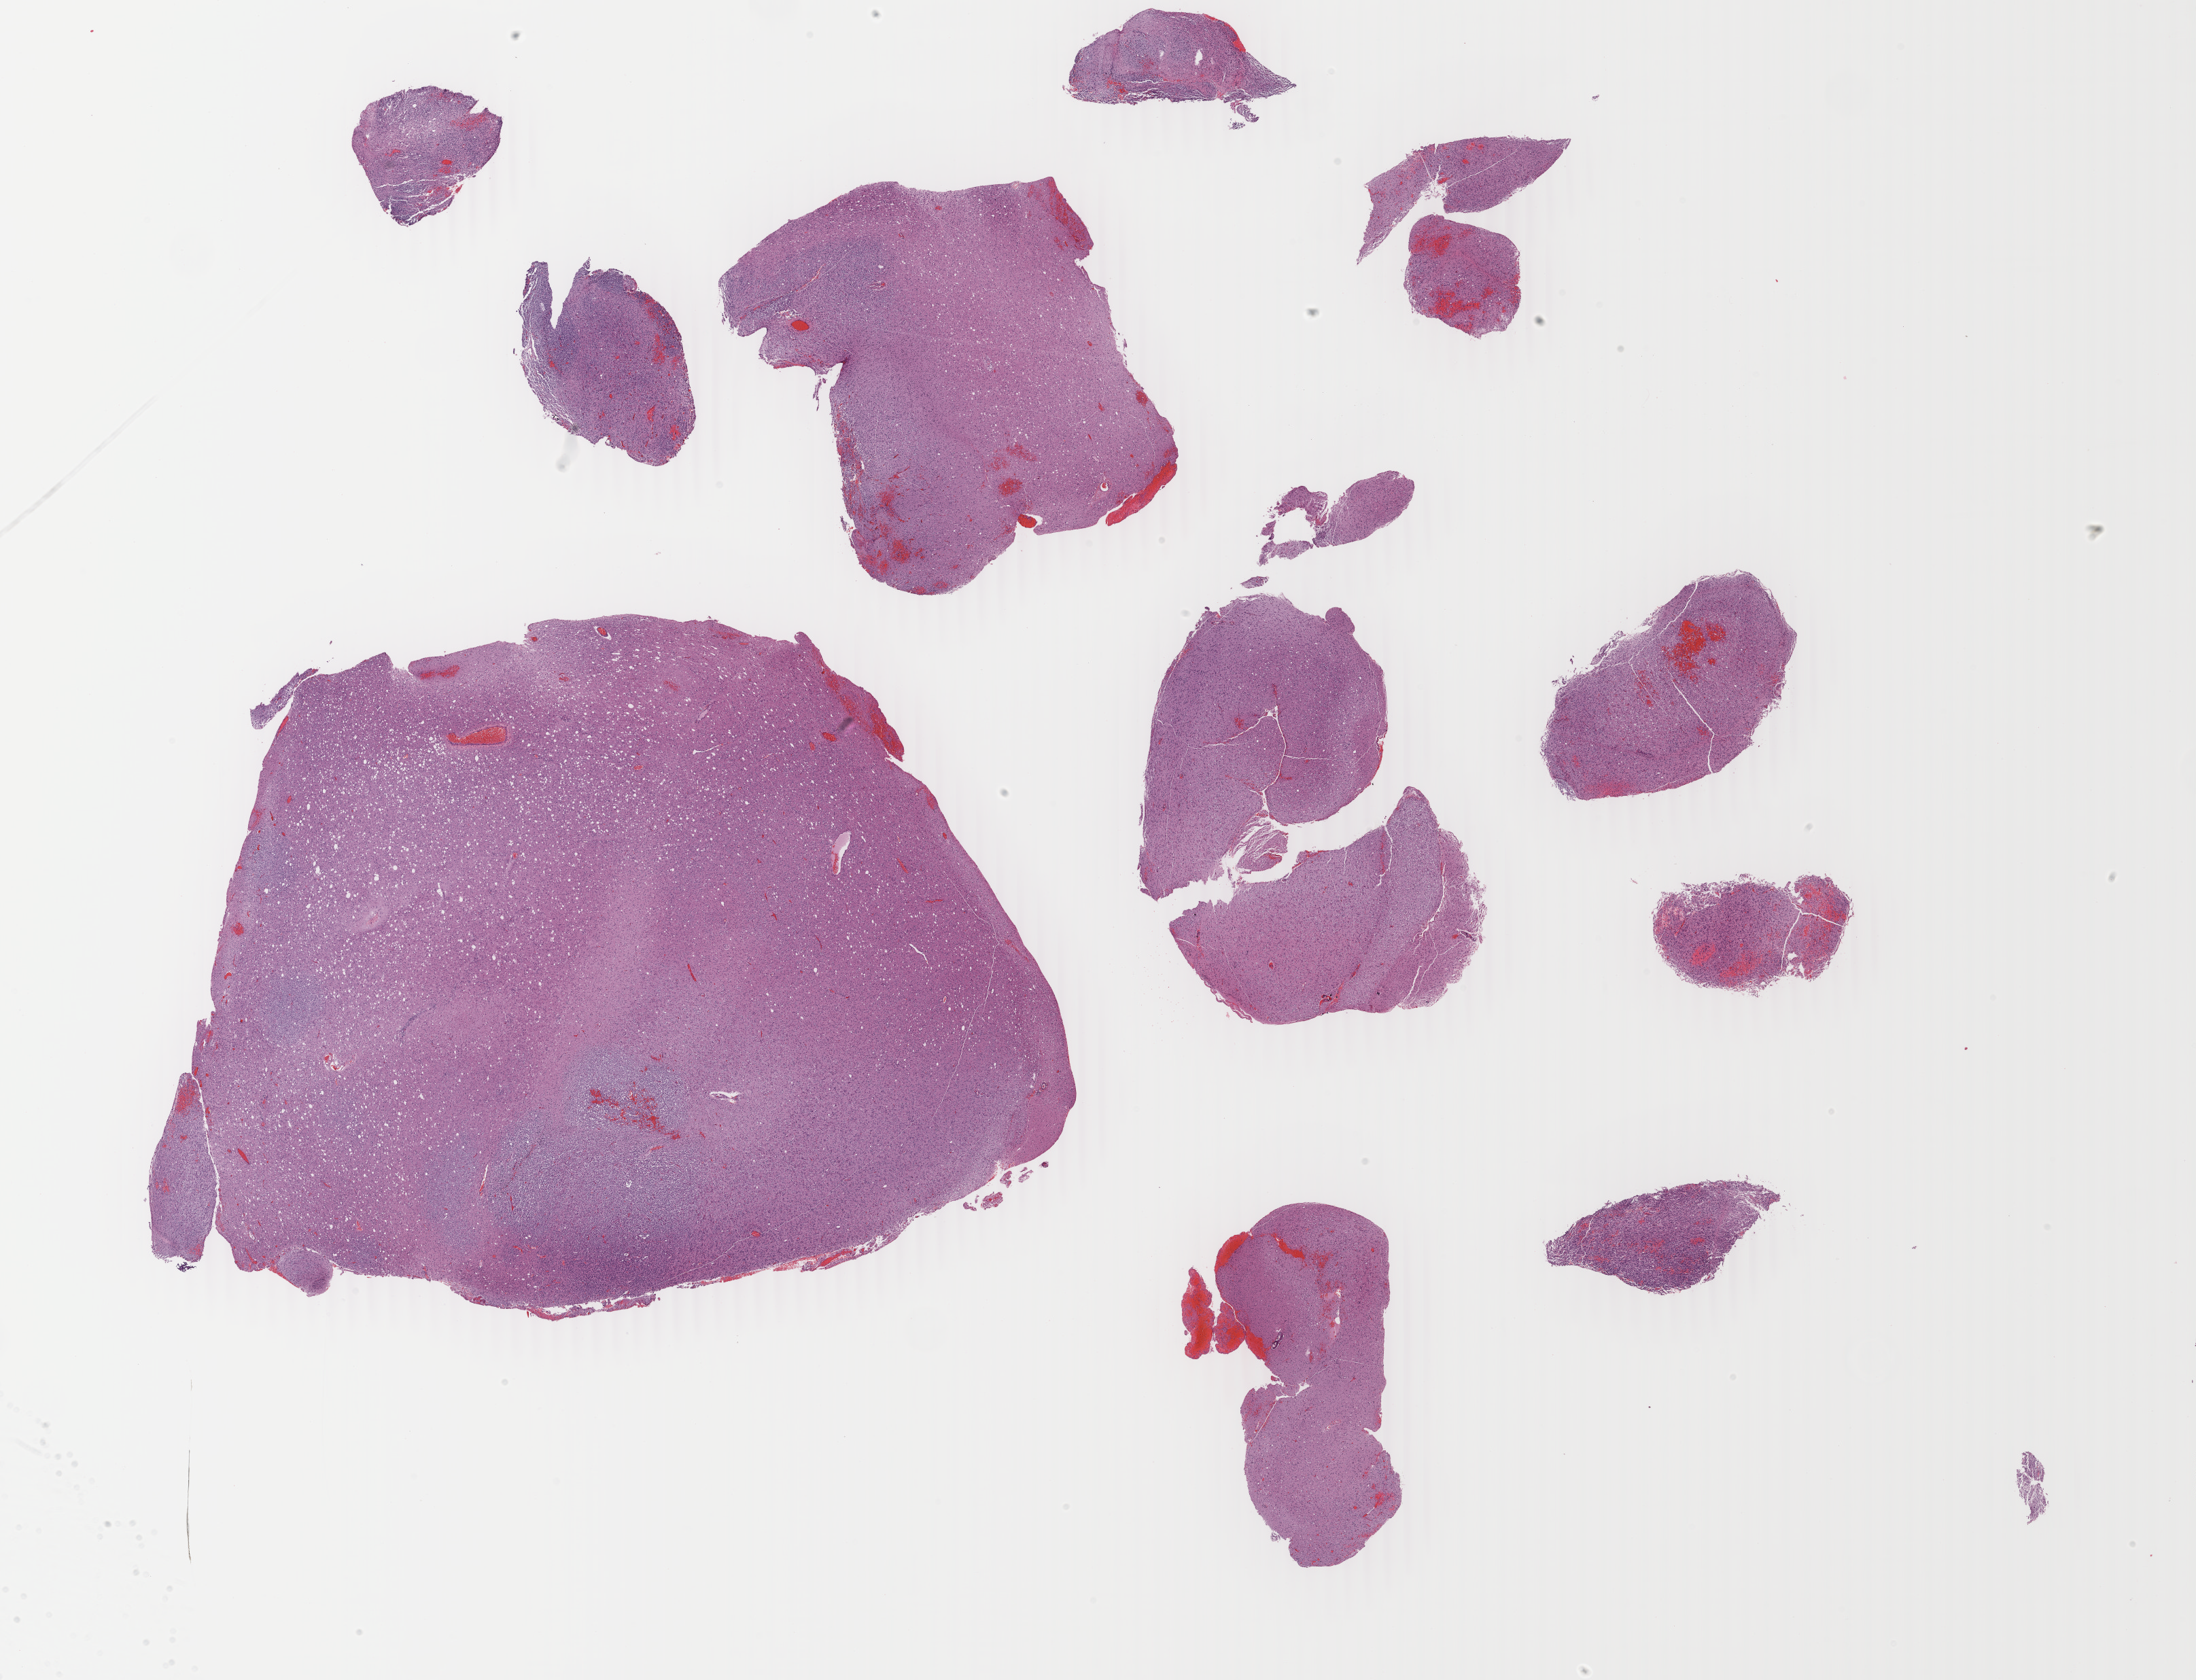
Digitized H&E tissue section (whole slide), whole scanned area (about 25.7 x 19.7 mm, acquisition: 40x scan) shown as a low-resolution overview; formalin-fixed paraffin-embedded (FFPE) diagnostic section; primary tumour sample from the brain. Female, age 38 years at initial diagnosis.
Histologic diagnosis: Oligodendroglioma, NOS (cerebrum).